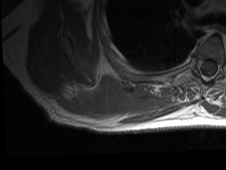
MRI of an extremity soft-tissue mass, one axial slice. Position 21 of 81 along the scan axis. MR volume resampled by the dataset authors to the PET/CT grid (not the native acquisition matrix). 226 × 170 image matrix, field of view 221 × 166 mm. Male patient. Case-level facts recorded for this patient, not image findings: histological type: pleiomorphic spindle cell undifferentiated; grade: high; site of the primary tumour: right parascapusular.
Structures marked on this image (expert contour drawn on MRI and transferred to this co-registered scan by the dataset authors):
- gross tumour volume including surrounding oedema: box from (x=57, y=78) to (x=182, y=125) px
- gross tumour volume (mass): (x=83, y=79)–(x=125, y=116)